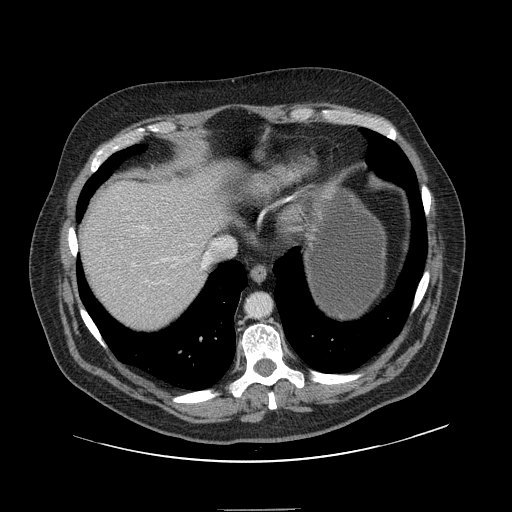
Contrast-enhanced abdominal CT, one axial slice; position 129 of 154 along the scan axis; 120 kVp; soft-tissue window (W 400 / L 40 HU); 512 × 512 image matrix. Male patient, age 61 years. Case-level facts recorded for this patient, not image findings: diagnosis: colorectal cancer liver metastases, imaged before liver resection; multiple liver metastases: yes.
Outlined on this slice (outlined manually by an expert reader):
- hepatic veins: bounding box [x1, y1, x2, y2] px = [162, 241, 216, 269]
- liver: [80, 165, 226, 332]
- planned liver remnant (the part of the liver to remain after resection): [80, 165, 226, 331]
- portal vein (with intrahepatic branches): [127, 216, 147, 282]